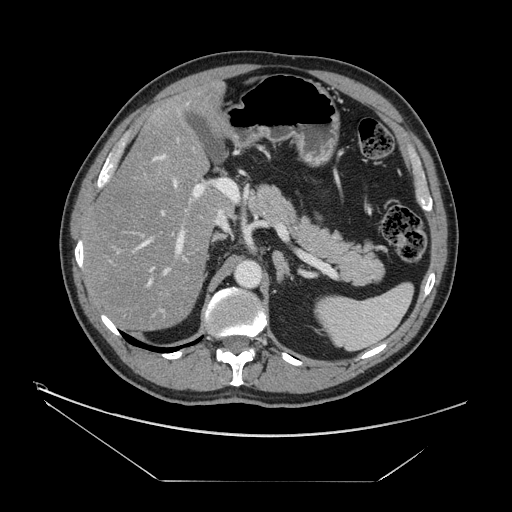
Contrast-enhanced abdominal CT, one axial slice; slice 88 of 161 in the series (ordered by position); 120 kVp; intravenous contrast given; soft-tissue window (W 400 / L 40 HU); 2.5 mm slice thickness; 512 × 512 image matrix. Male patient, age 65 years. From the clinical record (not read from this slice): diagnosis: colorectal cancer liver metastases, imaged before liver resection; multiple liver metastases: yes; largest metastasis: 4.2 cm; disease in both lobes: yes.
Structures marked on this image (manually delineated by an expert):
- hepatic veins: bounding box <140,178,178,287> (left, top, right, bottom; pixels)
- liver: <85,86,230,329>
- planned liver remnant (the part of the liver to remain after resection): <86,85,229,330>
- portal vein (with intrahepatic branches): <111,154,238,319>